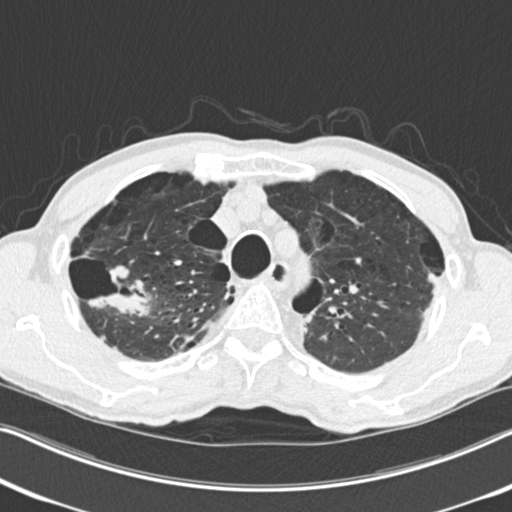
Low-dose screening chest CT, axial slice. Second annual screen. Lung window (W 1500 / L -600 HU). Male, age 71 years at enrolment. Current smoker at enrolment.
Expert reader's lesion annotation, bounding box (x1, y1, x2, y2) in pixels: (78, 255, 153, 321). The screening reader recorded 4 non-calcified nodules or masses ≥4 mm on this exam; which of them this box marks is not recorded. Official screen result: positive, change unspecified: nodule(s) >= 4 mm or enlarging nodule(s), mass(es), or other non-specific abnormalities suspicious for lung cancer. Lung cancer was diagnosed 83 days after this screen: adenocarcinoma, NOS, right upper lobe, well differentiated (G1), stage IA (AJCC 6th edition), 30 mm at pathology.